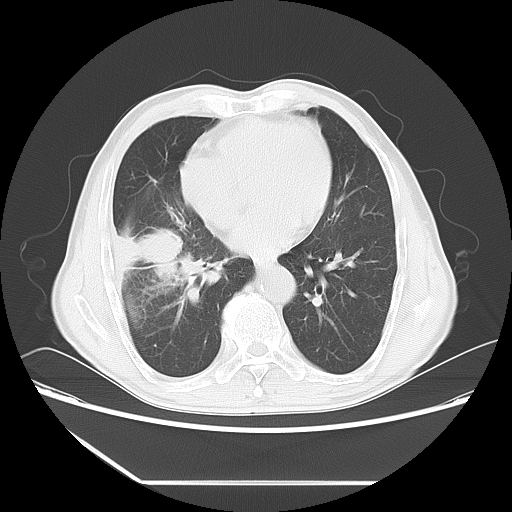
Chest CT, one axial slice. Slice 25 of 60 in the series (ordered by position). Reconstruction kernel LUNG. Lung window (W 1500 / L -600 HU). 5 mm slice thickness. 512 × 512 image matrix. Patient: male, 72 years. From the clinical record (not read from this slice): clinical TNM (as recorded): T1c N0 M0.
Structures marked on this image (rectangle marked by the reading radiologist):
- lung tumour (recorded histology: squamous cell carcinoma): box from (x=122, y=210) to (x=193, y=285) px